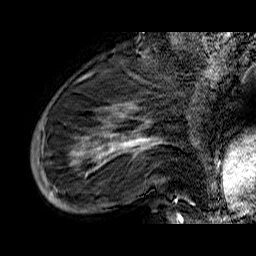
Breast MRI (dynamic contrast-enhanced), one sagittal slice. Position 16 of 60 along the scan axis. Dynamic contrast-enhanced series, time point 2 of 6 at this slice position (early post-contrast). 1.5 T. TE 6.5 ms, TR 32.9 ms. 4 mm slice thickness. 256 × 256 image matrix. Female patient. Case-level facts recorded for this patient, not image findings: setting: breast cancer imaged before/during neoadjuvant chemotherapy; receptor status: HR-positive, HER2-negative.
Annotated regions visible in this slice (semi-automatic segmentation, software-assisted and operator-edited):
- analysis volume of interest (the breast-tissue region the enhancement analysis was run in; not a lesion): bounding box <33,74,176,210> (left, top, right, bottom; pixels)
- tumour enhancement mask (voxels above the 100 % enhancement threshold inside the analysis volume of interest): <37,104,176,203>